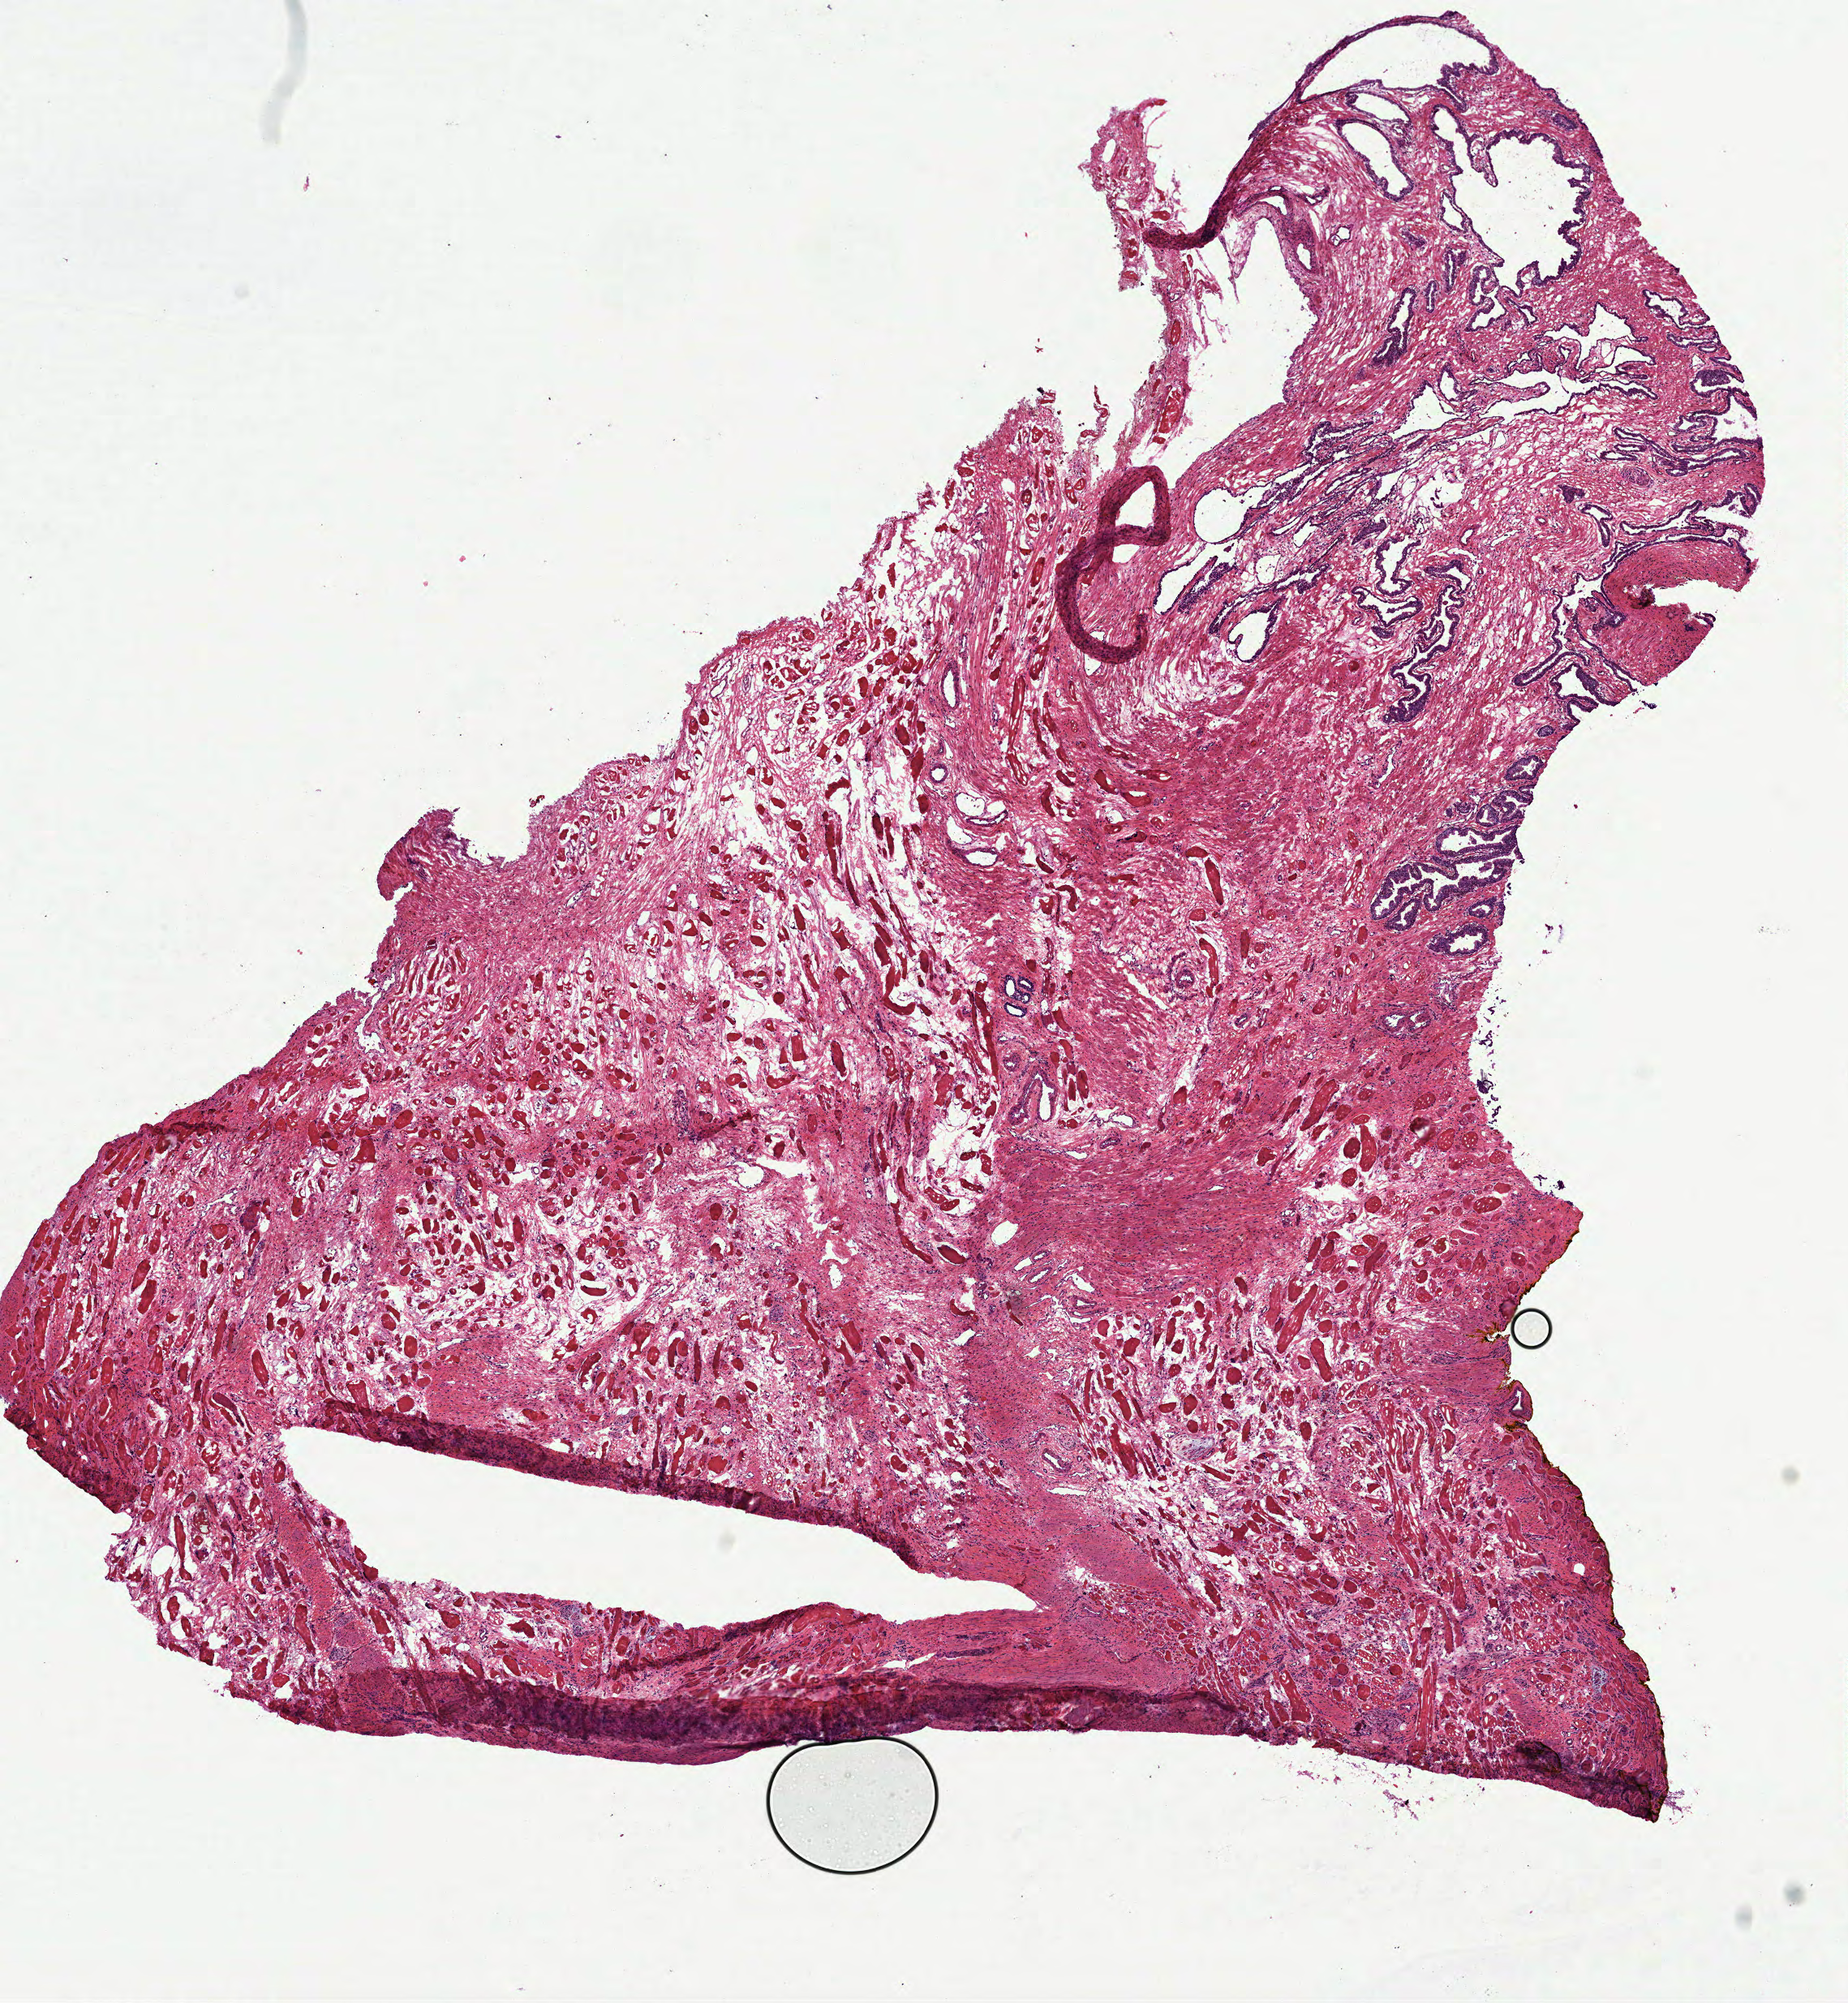
Whole-slide histology image, Hematoxylin and eosin (H&E) stained — a low-resolution overview of the entire scanned area, about 9.2 x 10.0 mm; frozen section from the top of the tissue portion; prostate, solid tissue normal (non-tumour tissue) sample. Male, age 53 years at initial diagnosis.
This section: solid tissue normal sample (biorepository sample class). Patient diagnosis: Acinar cell carcinoma (prostate gland).